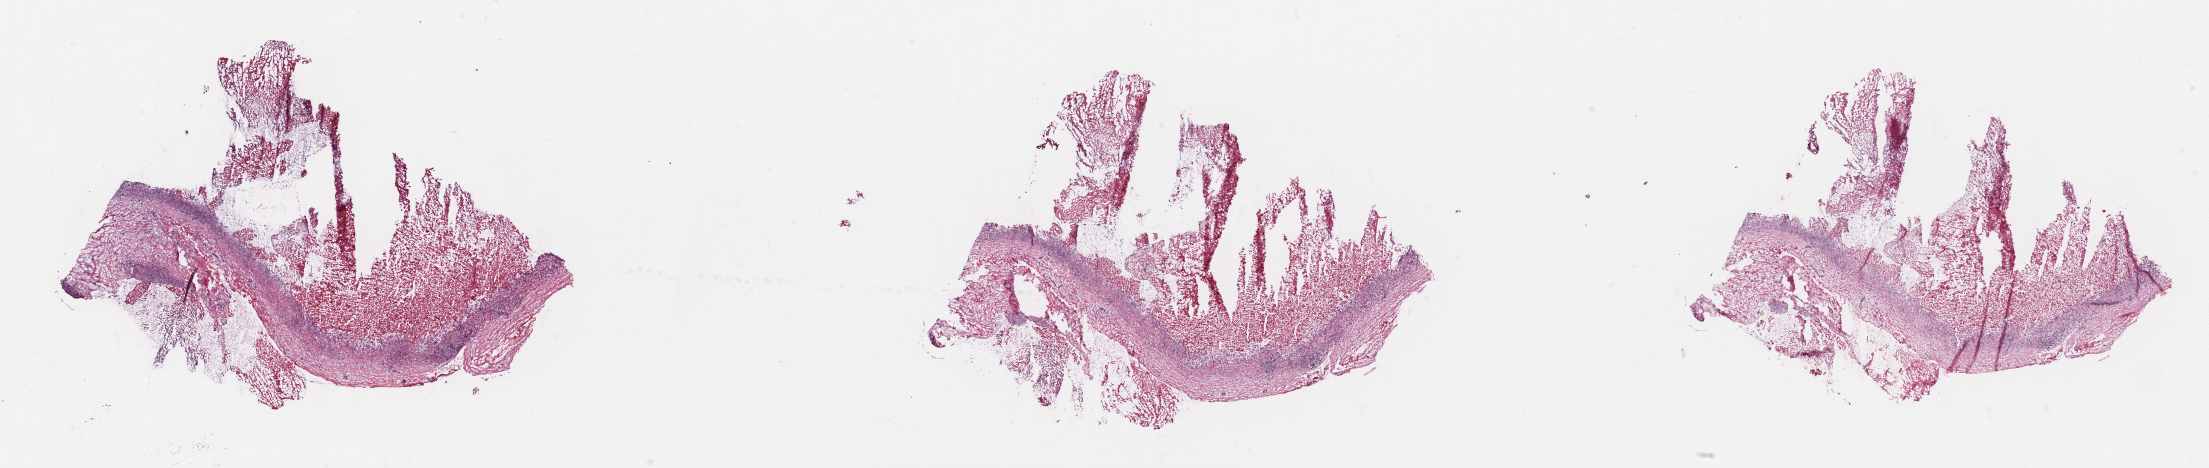
Whole-slide image, hematoxylin and eosin (H&E) stain, shown as a low-resolution overview of the whole scanned area (about 35.7 x 7.6 mm), cryosection, primary tumor, site: lymph node of head and neck. Male, age 5 years at initial diagnosis. Composition of this section per pathologist review: tumor cells 60%, tumor nuclei 90%, stromal cells 30%, necrosis 10%, normal cells 0%. Inflammatory infiltration, as recorded: lymphocyte infiltration 3%, monocyte infiltration 0%, neutrophil infiltration 0%.
Section: bottom of the tissue portion. Ann Arbor stage (patient): Stage I. Histologic diagnosis: Burkitt lymphoma, NOS.